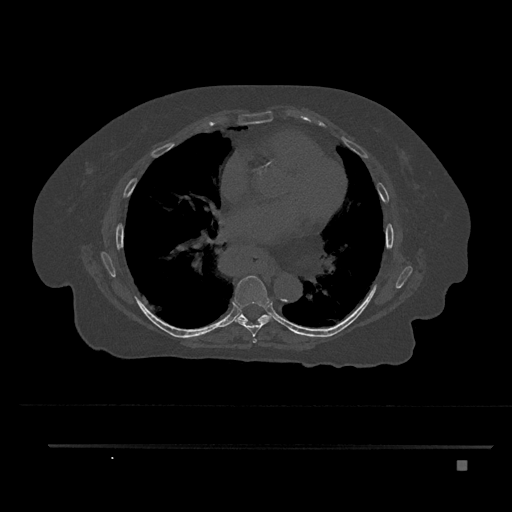
CT including the spine, one axial slice. Slice 470 of 797 in the series (ordered by position). Reconstruction kernel Br40s/3. 120 kVp. Bone window (W 1800 / L 400 HU). 0.5 mm slice thickness. 512 × 512 image matrix, field of view 437 × 437 mm. Female patient, age 76 years. Case-level facts recorded for this patient, not image findings: primary cancer: lung.
Annotated regions visible in this slice (semi-automatic segmentation, software-assisted and operator-edited):
- T6 vertebra: bounding box (x1, y1, x2, y2) in pixels: (252, 339, 257, 343)
- T7 vertebra: (234, 275, 273, 337)
- T8 vertebra: (237, 313, 270, 321)